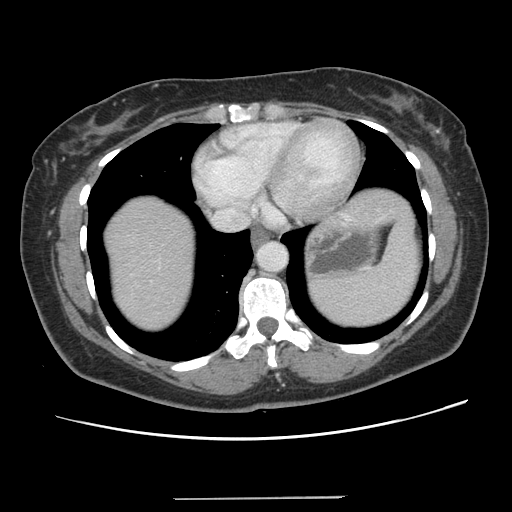
Contrast-enhanced abdominal CT, one axial slice; position 122 of 141 along the scan axis; 120 kVp; intravenous contrast given; soft-tissue window (W 400 / L 40 HU); 2.5 mm slice thickness; 512 × 512 image matrix, field of view 366 × 366 mm. Female patient, age 53 years. Case-level facts recorded for this patient, not image findings: diagnosis: colorectal cancer liver metastases, imaged before liver resection; multiple liver metastases: no; largest metastasis: 14.5 cm; disease in both lobes: yes.
Structures marked on this image (outlined manually by an expert reader):
- hepatic veins: bounding box [x1, y1, x2, y2] px = [156, 210, 238, 266]
- liver: [102, 188, 408, 332]
- planned liver remnant (the part of the liver to remain after resection): [103, 214, 196, 332]